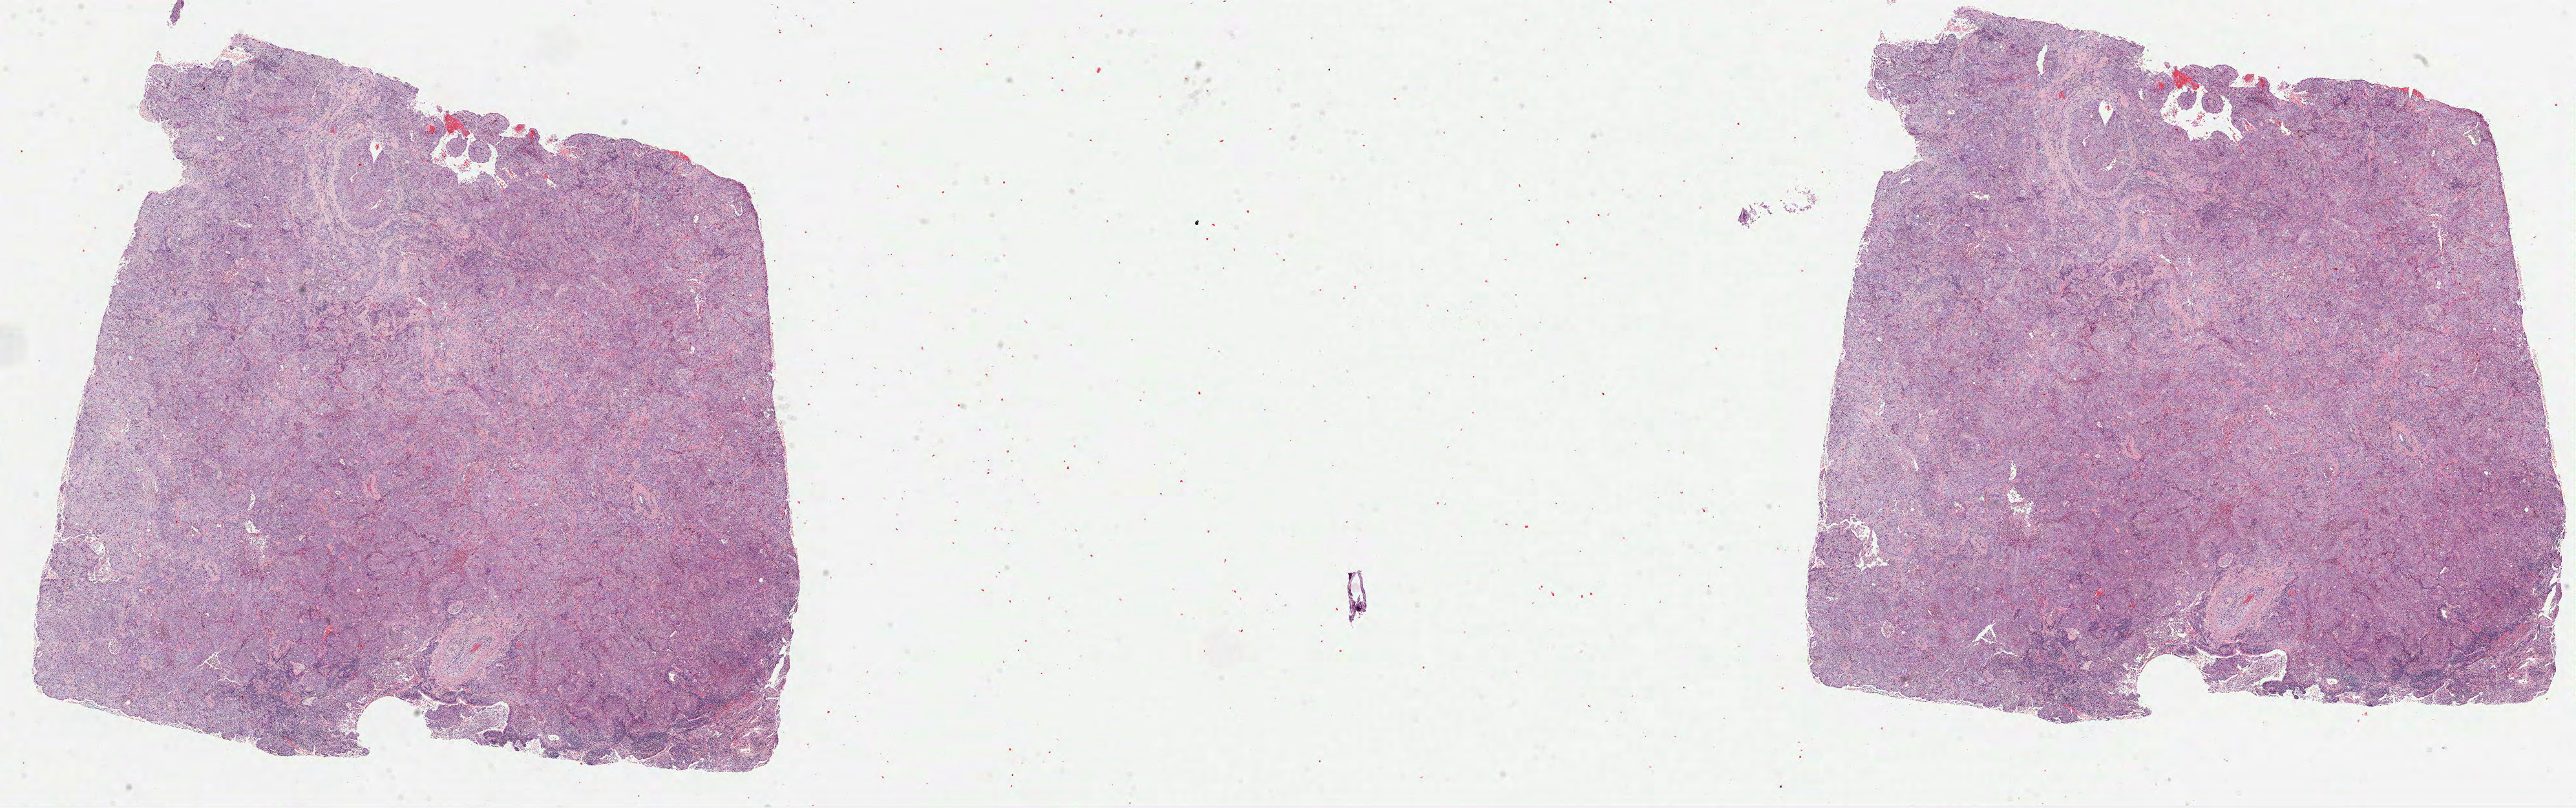
Whole-slide histology image, H&E — a low-resolution overview of the entire scanned area, about 32.1 x 10.1 mm. Formalin-fixed paraffin-embedded (FFPE) diagnostic section. Primary tumour sample from the lung. Patient: male, age at initial diagnosis 71 years.
• AJCC pathologic stage: IIB
• diagnosis: Squamous cell carcinoma, NOS (lower lobe, lung)